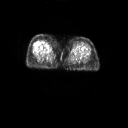
FDG PET of an extremity soft-tissue mass (from a PET/CT study), one axial slice. Slice 10 of 267 in the series (ordered by position). 3.27 mm slice thickness. 128 × 128 image matrix, field of view 700 × 700 mm. Female patient, age 56 years. From the clinical record (not read from this slice): histological type: malignant solitary fibrous tumor; grade: intermediate; site of the primary tumour: right thigh.
Annotated regions visible in this slice (expert contour drawn on MRI and transferred to this co-registered scan by the dataset authors):
- gross tumour volume including surrounding oedema: bounding box [x1, y1, x2, y2] px = [42, 42, 51, 47]